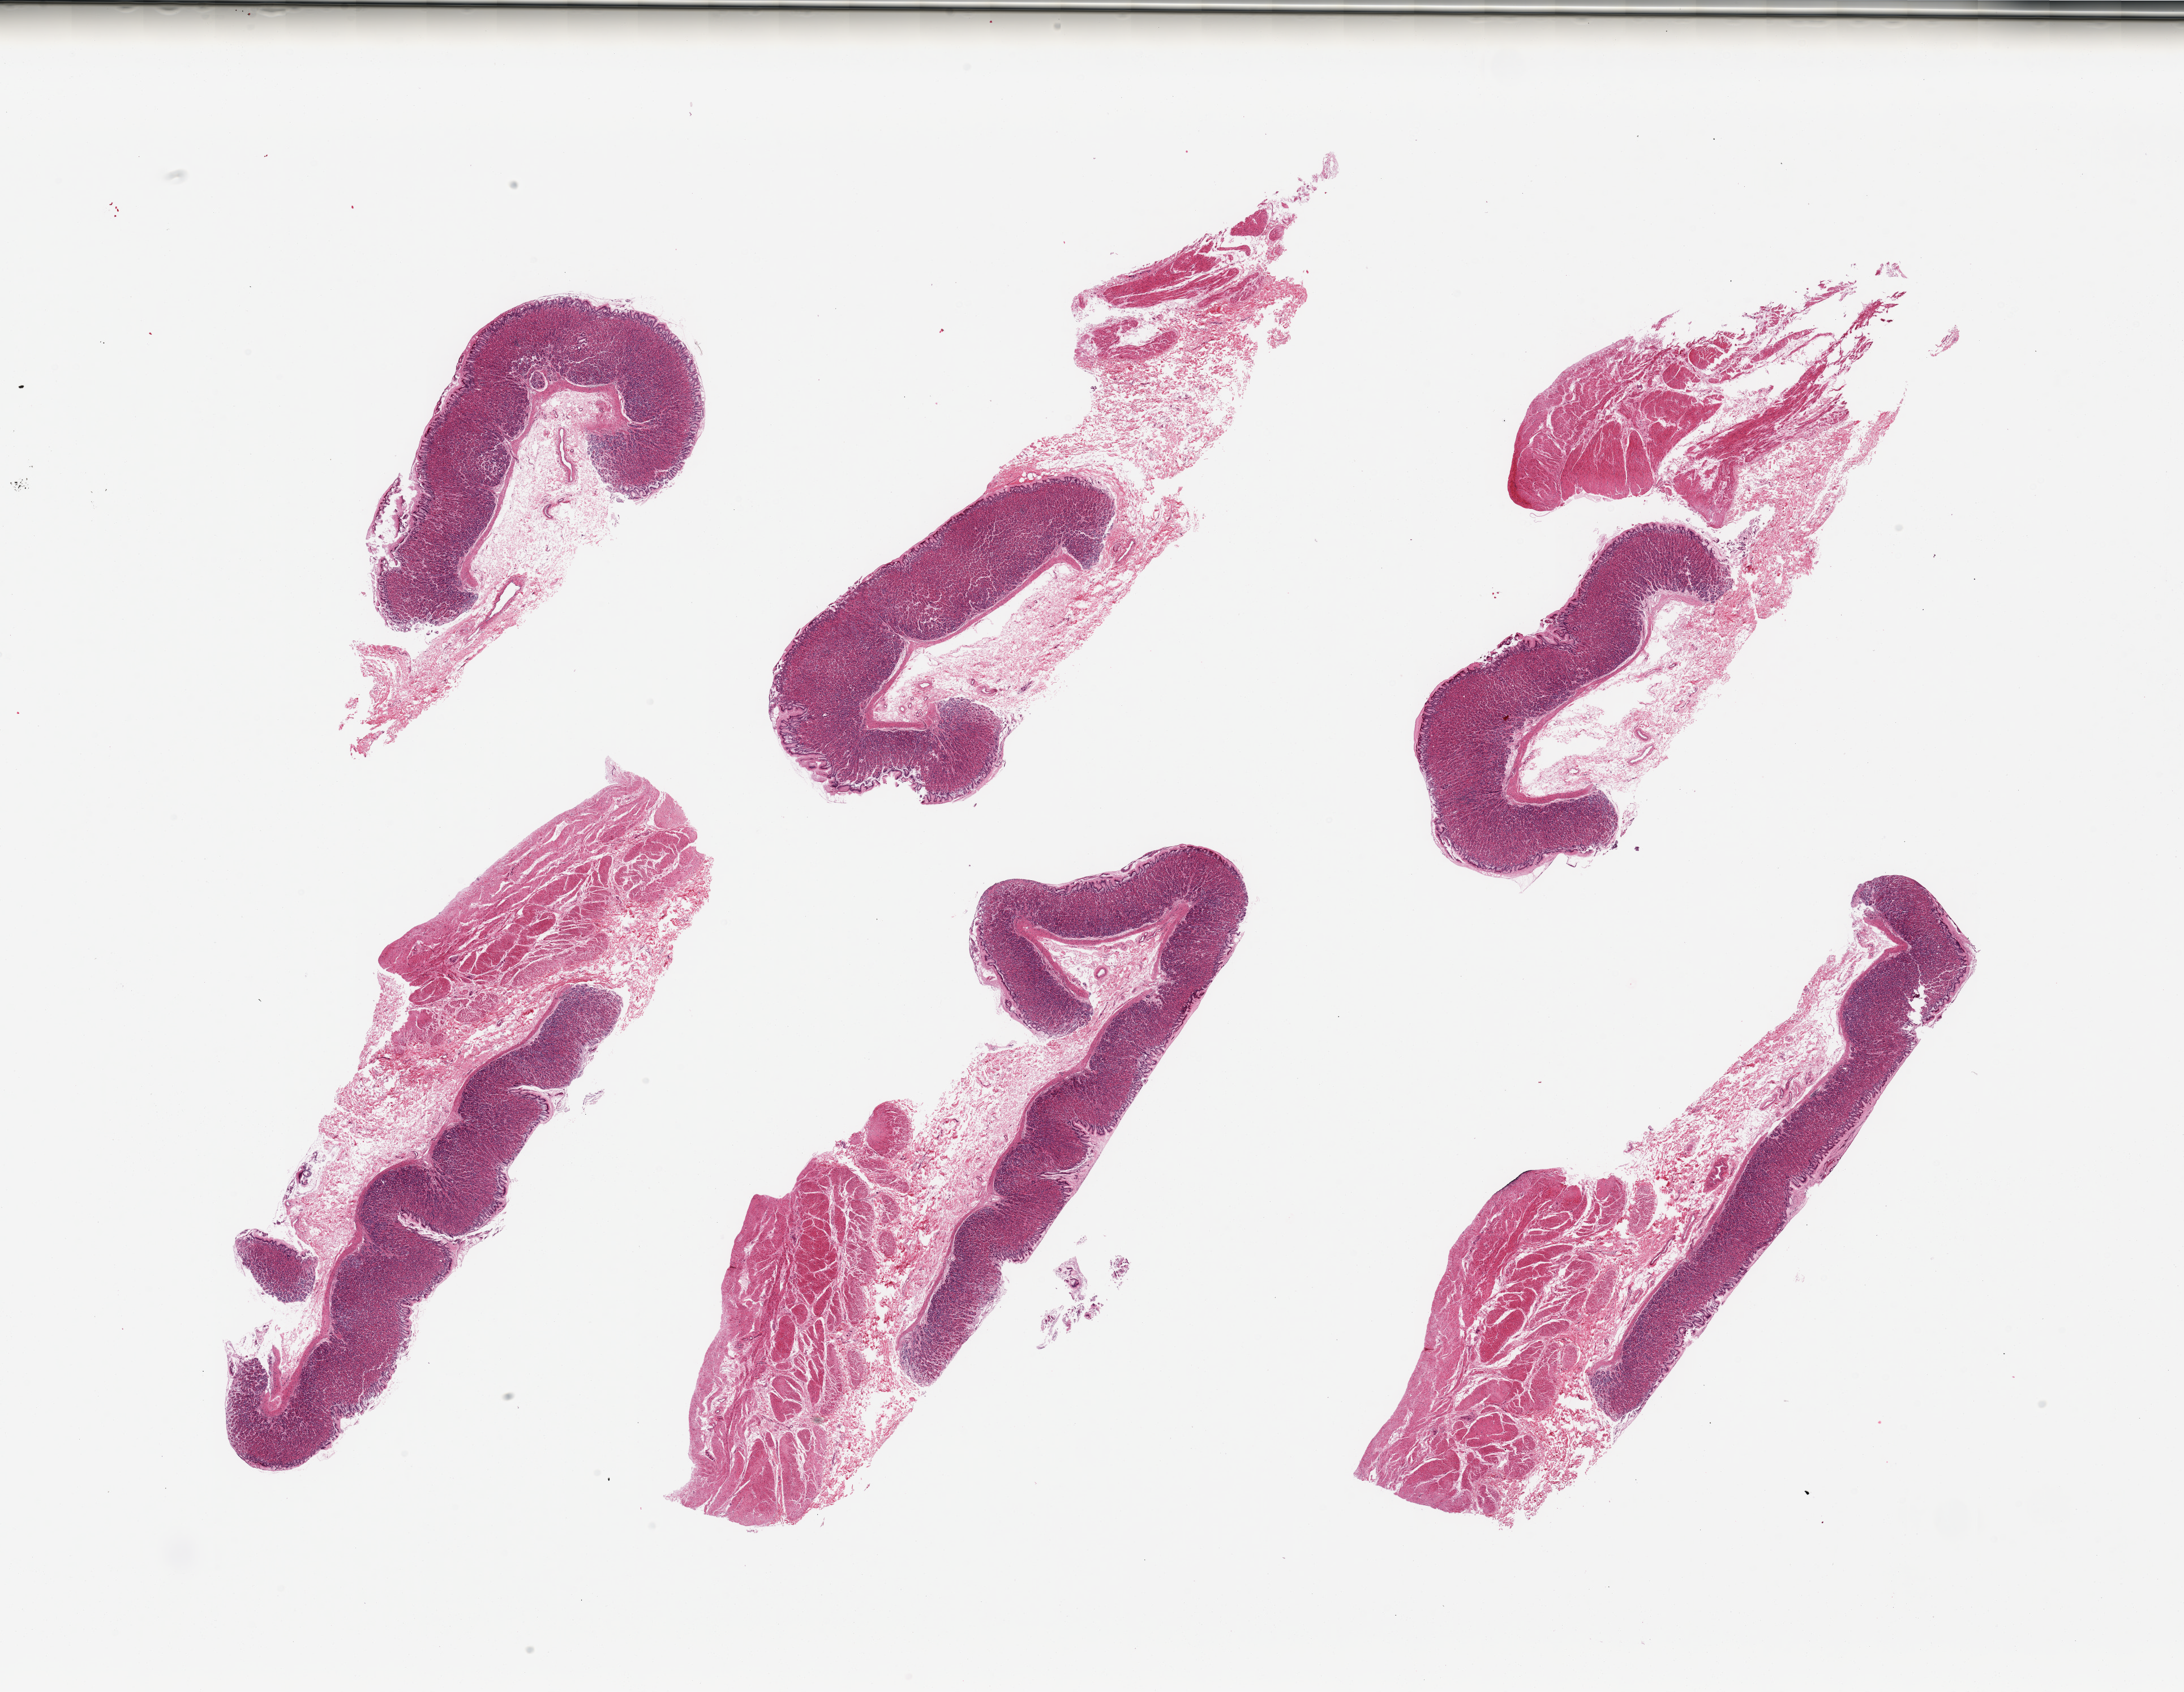
Digitized haematoxylin and eosin-stained section, low-resolution overview of the scanned area, about 30.5 x 23.6 mm; PAXgene-fixed, paraffin-embedded tissue; section of stomach (target tissue); tissue donor sample. Male donor.
Pathologist's review note for this sample: 6 pieces, target mucosa extremely well preserved, good specimen, ~40-60% thickness.